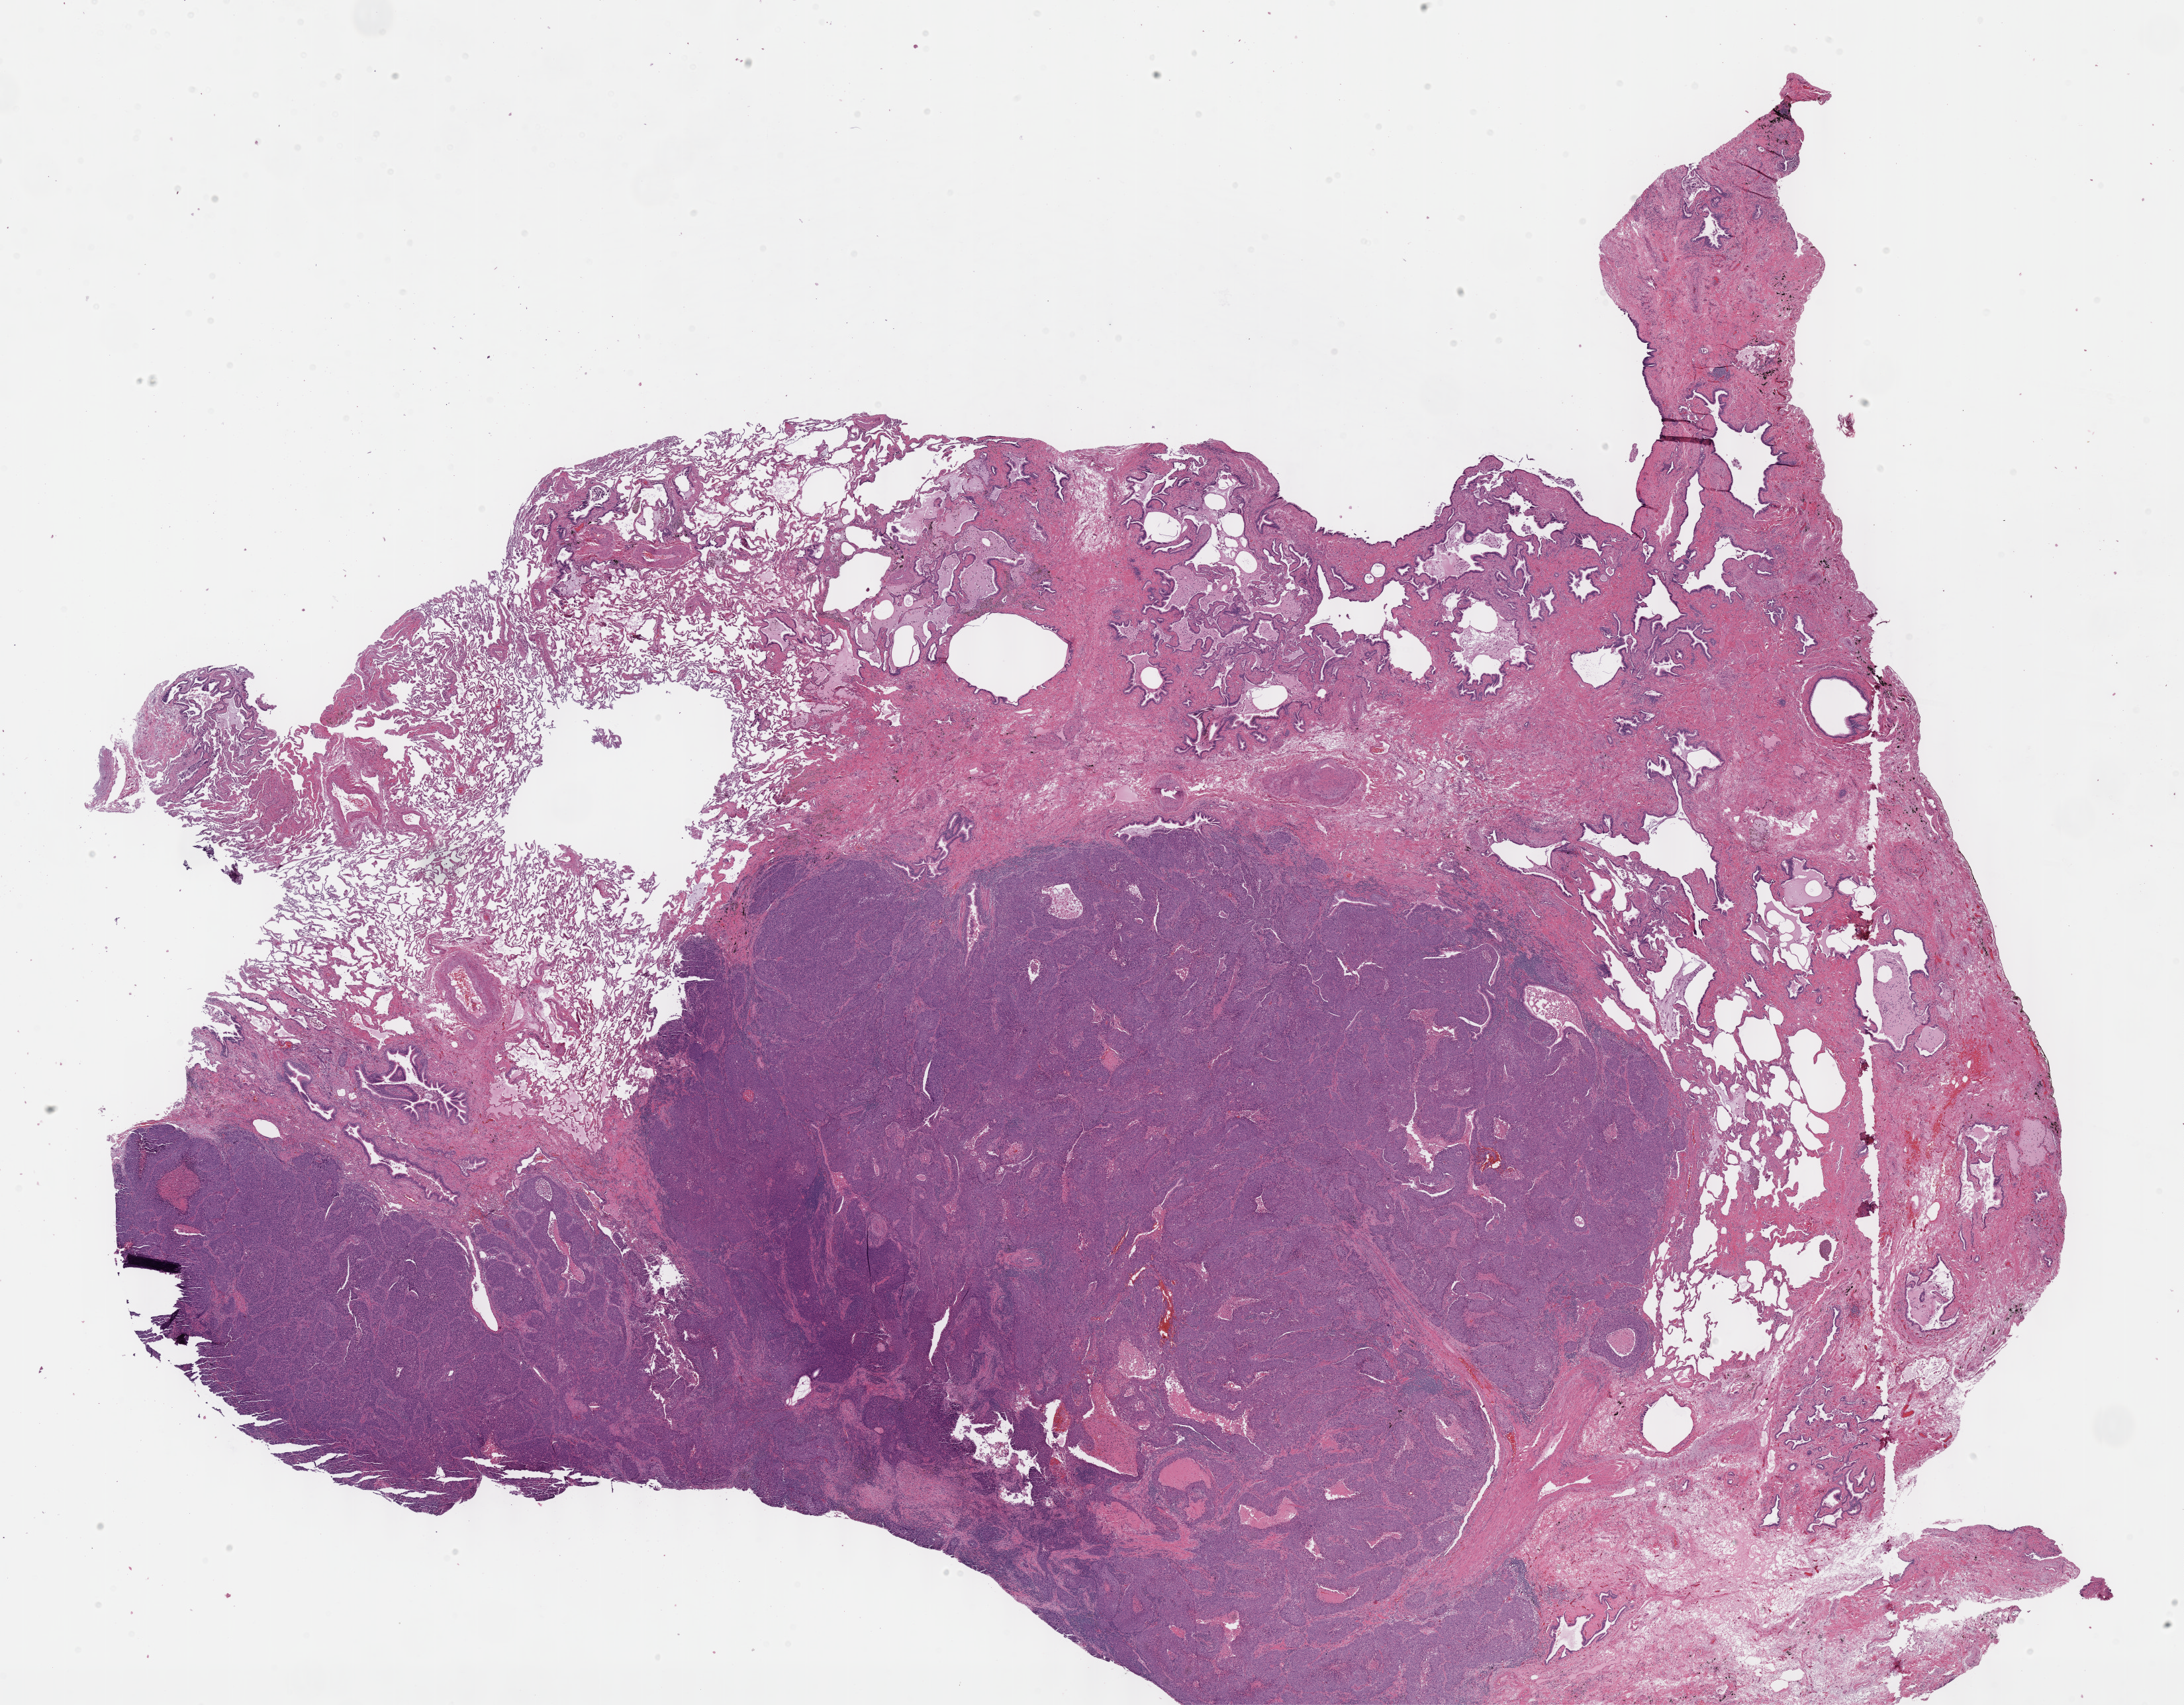
Whole-slide histology image, H&E, low-resolution overview of the scanned area, about 26.7 x 20.8 mm (from a 40x scan). Formalin-fixed paraffin-embedded (FFPE) diagnostic section. Lung, primary tumour sample. Male, age 65 years at initial diagnosis.
* AJCC pathologic stage: IA
* histologic diagnosis: Squamous cell carcinoma, NOS (lower lobe, lung)